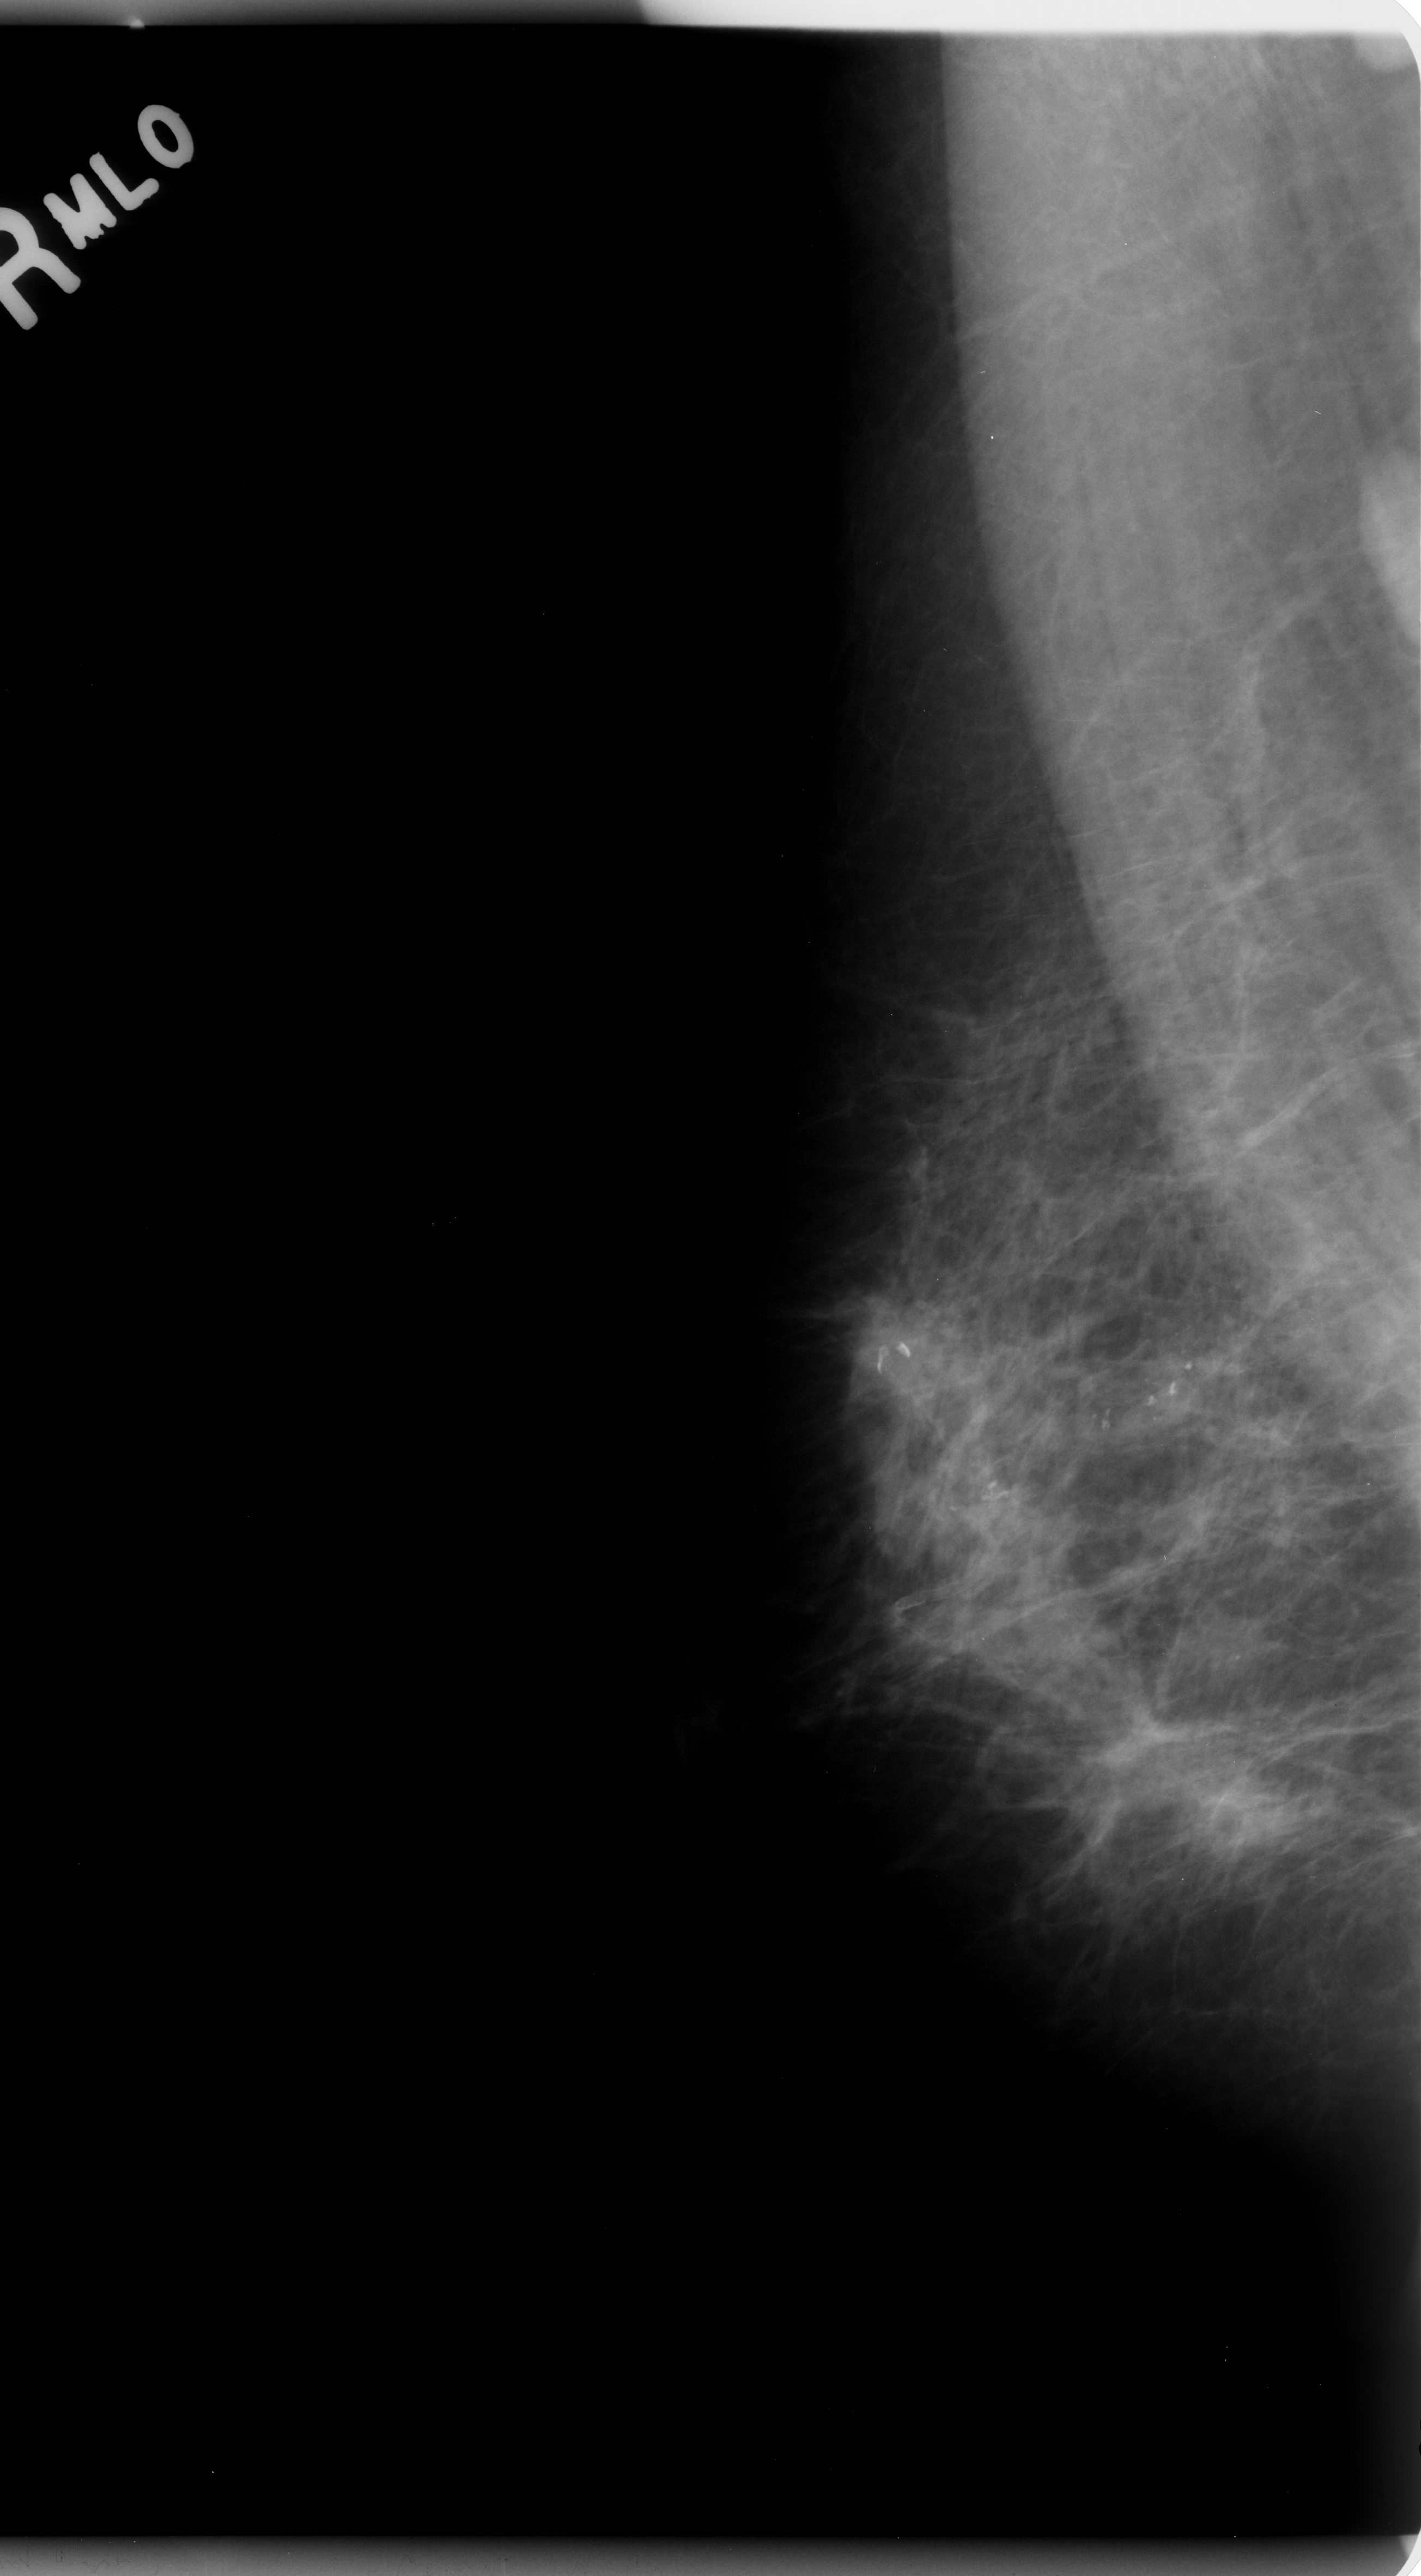
Scanned film-screen mammogram, right breast, MLO view.
- Calcifications, morphology pleomorphic, distribution segmental; BI-RADS assessment category 5; pathology result (as recorded, not read from the image): malignant.